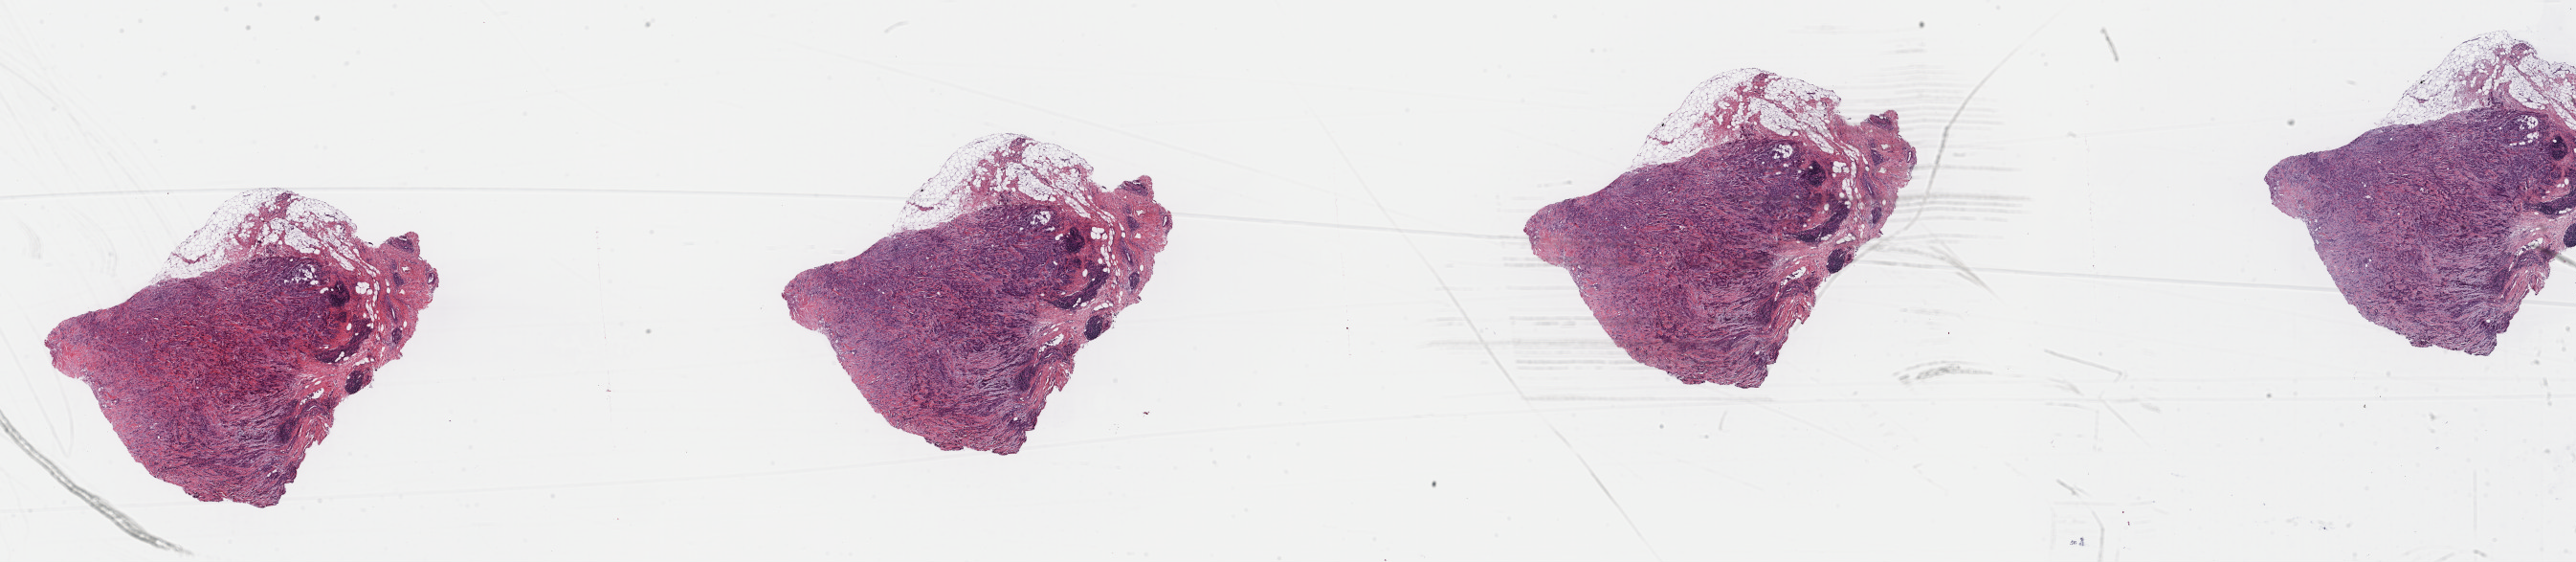
H&E-stained whole-slide image, shown as a low-resolution overview of the whole scanned area (about 42.5 x 9.3 mm), FFPE section, breast, primary tumour sample. Patient: female, age at initial diagnosis 56 years.
- lymph nodes positive (case pathology): 0 of 4 examined
- AJCC pathologic stage: IIA
- TNM: T2 N0 (i-) M0
- histologic diagnosis: Infiltrating duct carcinoma, NOS